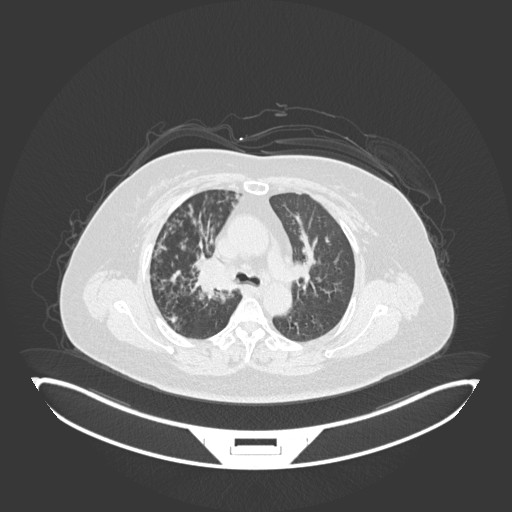
Chest CT, one axial slice. Reconstruction kernel B30f. 120 kVp. Lung window (W 1500 / L -600 HU). 512 × 512 image matrix, field of view 500 × 500 mm. Patient: female, 60 years. Case-level facts recorded for this patient, not image findings: clinical TNM (as recorded): T1c N0 M0; histopathological grade: G1-G2.
Structures marked on this image (rectangle marked by the reading radiologist):
- lung tumour (recorded histology: squamous cell carcinoma): bounding box <193,255,240,296> (left, top, right, bottom; pixels)